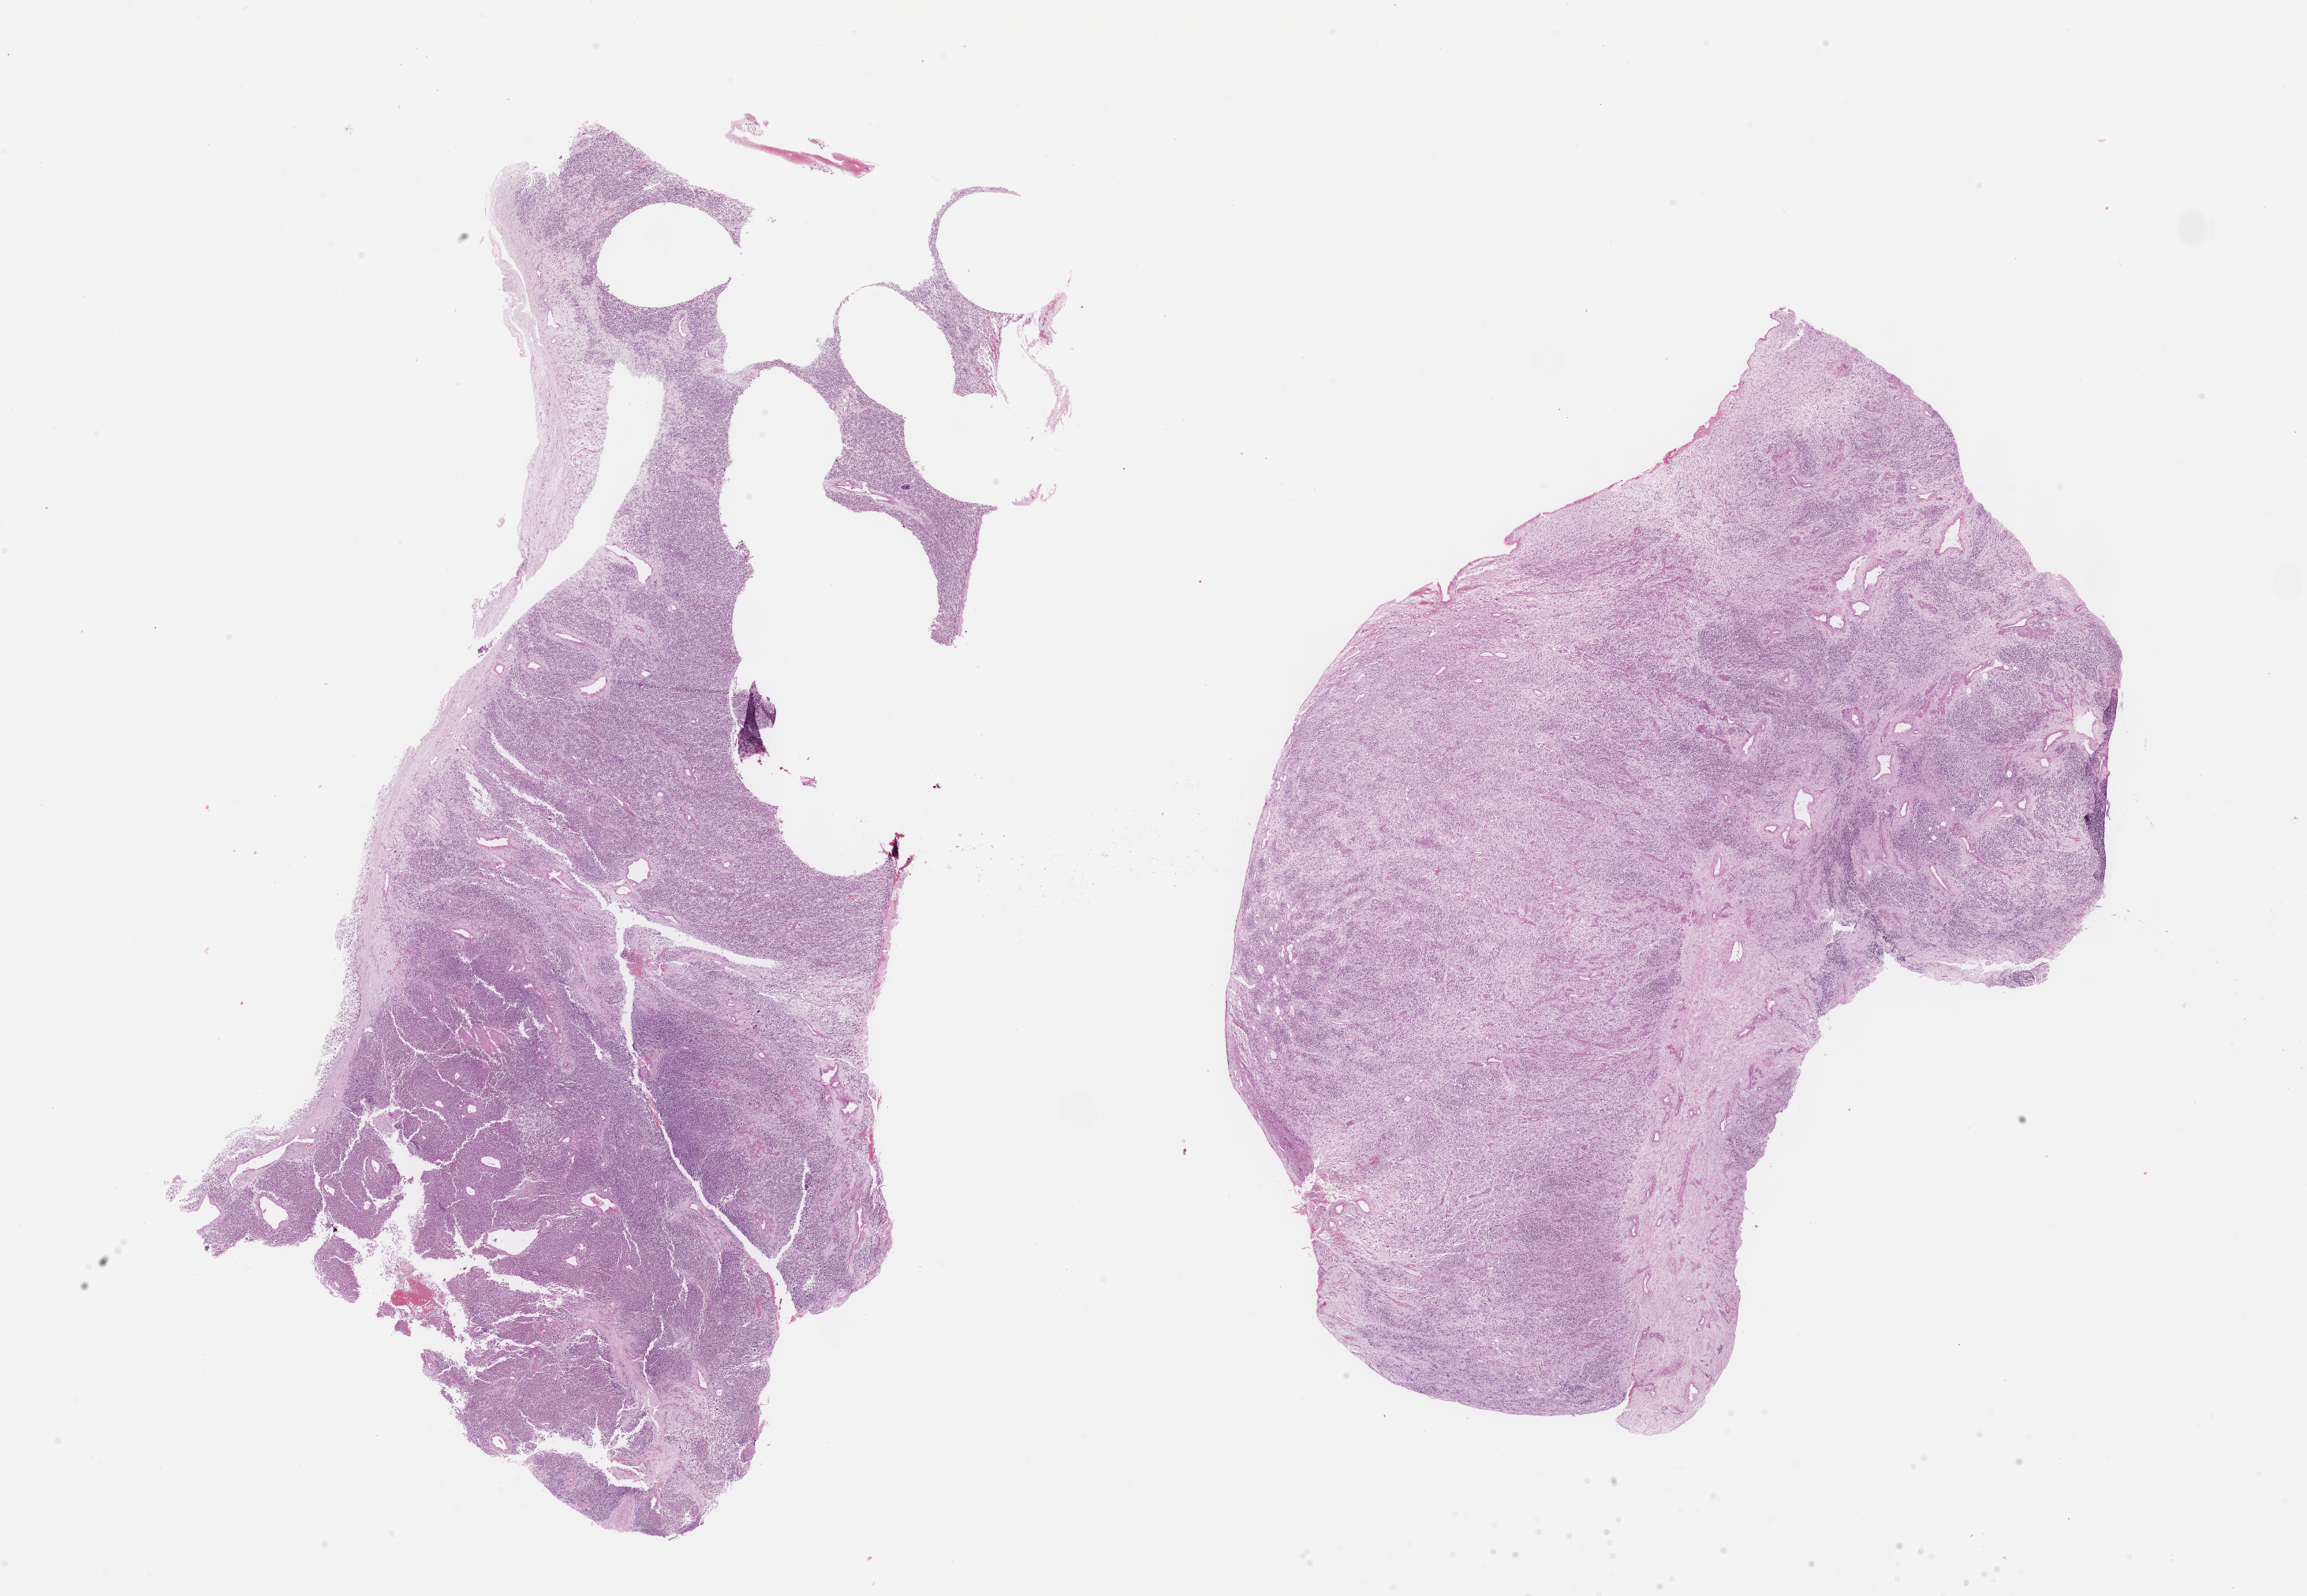
Digitized haematoxylin and eosin-stained section of tumor tissue — a low-resolution overview of the entire scanned area, about 23.6 x 16.4 mm; formalin-fixed paraffin-embedded section; sample anatomic site: abdomen. Patient: female, age 6.2 years at diagnosis.
* stage (as recorded): 3
* primary site (case record): retroperitoneum
* metastatic status at presentation (as recorded): non-metastatic (unconfirmed)
* diagnosis: rhabdomyosarcoma; histological classification: embryonal rhabdomyosarcoma